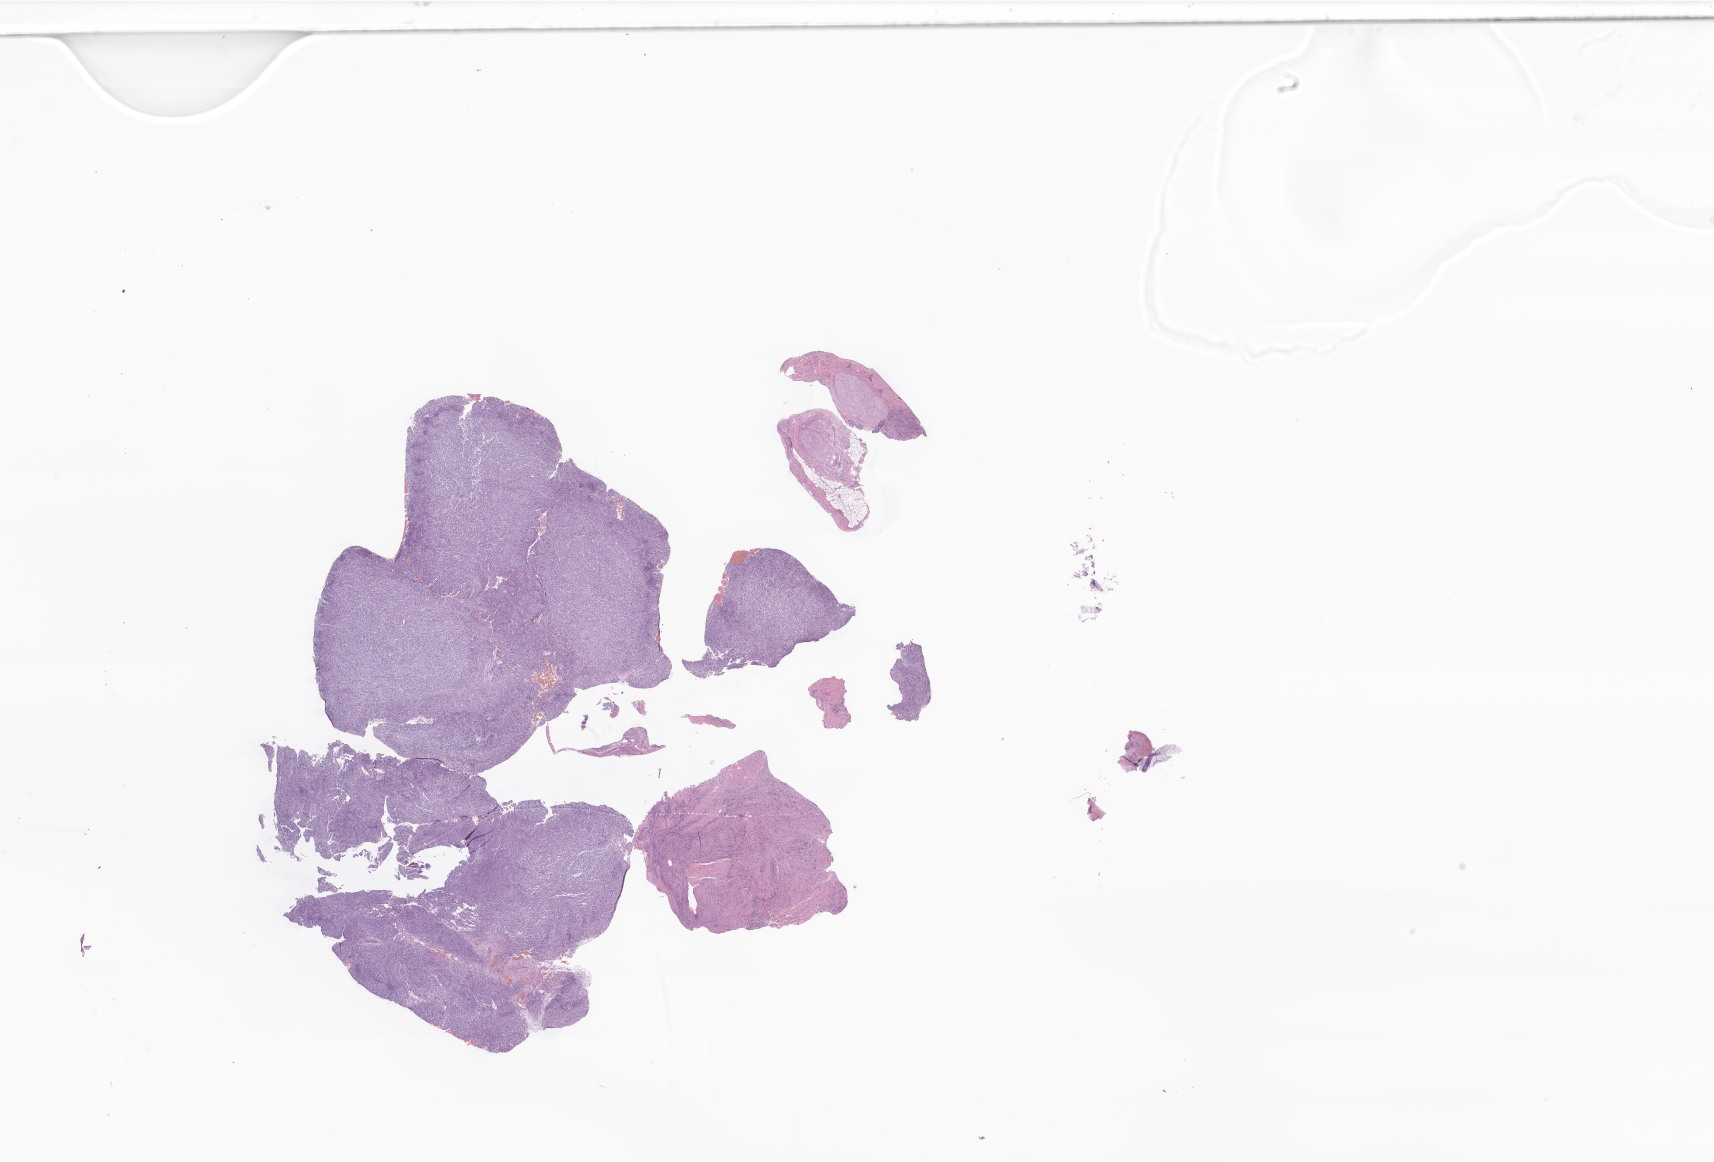
Haematoxylin and eosin whole-slide image of tumor tissue from the soft tissues of head and neck, whole scanned area (about 28.9 x 19.6 mm) shown as a low-resolution overview. FFPE section. Patient female; age 37 months (3 years 1 month).
Recorded diagnosis: Embryonal rhabdomyosarcoma, NOS.